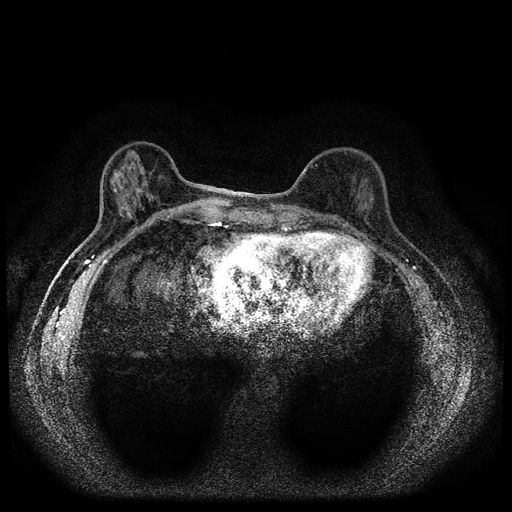
Breast MRI (dynamic contrast-enhanced, multi-phase), one axial slice; slice 33 of 112 in the series (ordered by position); dynamic contrast-enhanced series, time point 2 of 5 at this slice position (early post-contrast); 1.5 T; TE 2.7 ms, TR 5.4 ms; 2 mm slice thickness; 512 × 512 image matrix, field of view 320 × 320 mm. Patient: female, 61 years.
Outlined on this slice (semi-automatic segmentation, software-assisted and operator-edited):
- breast lesion (labelled benign in the annotation): bounding box [x1, y1, x2, y2] px = [110, 170, 156, 220]